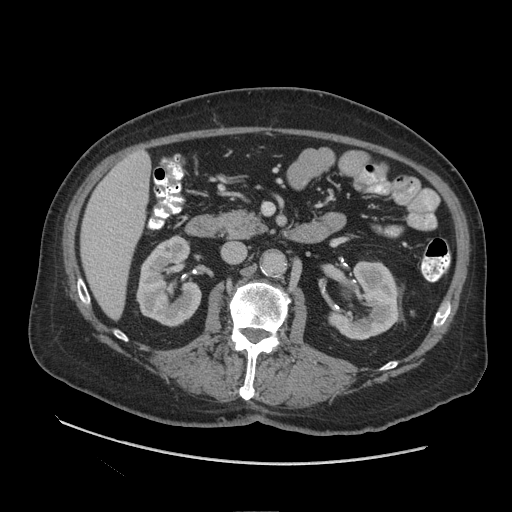
Contrast-enhanced abdominal CT (liver protocol), one axial slice; position 36 of 109 along the scan axis; 140 kVp; soft-tissue window (W 400 / L 40 HU); 512 × 512 image matrix, field of view 420 × 420 mm. From the clinical record (not read from this slice): diagnosis: hepatocellular carcinoma (patient treated with transarterial chemoembolisation; whether this scan precedes or follows treatment is not stated here); TNM stage (as recorded): Stage-I; Child-Pugh class: A; tumour nodularity: uninodular.
Outlined on this slice (semi-automatically segmented with operator editing):
- liver parenchyma outside the tumour (the mass and vessels are separate outlines, so this box may not span the whole liver): box from (x=80, y=152) to (x=150, y=318) px